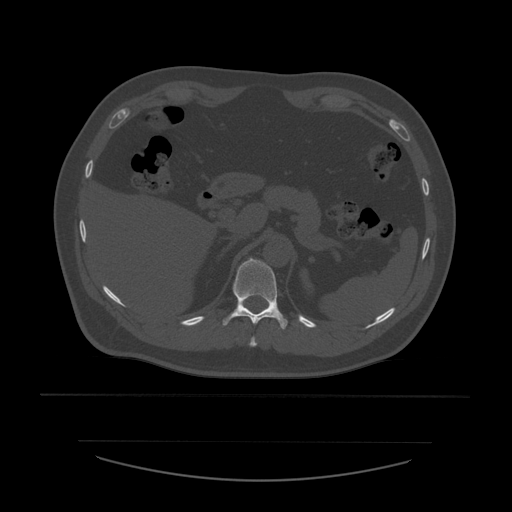
CT including the spine, one axial slice; slice 275 of 532 in the series (ordered by position); reconstruction kernel STANDARD; 120 kVp; bone window (W 1800 / L 400 HU); 1.25 mm slice thickness; 512 × 512 image matrix, field of view 441 × 441 mm. Patient age 44 years. Case-level facts recorded for this patient, not image findings: primary cancer: soft tissue sarcoma.
Outlined on this slice (semi-automatic segmentation, software-assisted and operator-edited):
- T10 vertebra: bounding box [x1, y1, x2, y2] px = [249, 337, 257, 347]
- T11 vertebra: [223, 258, 288, 330]